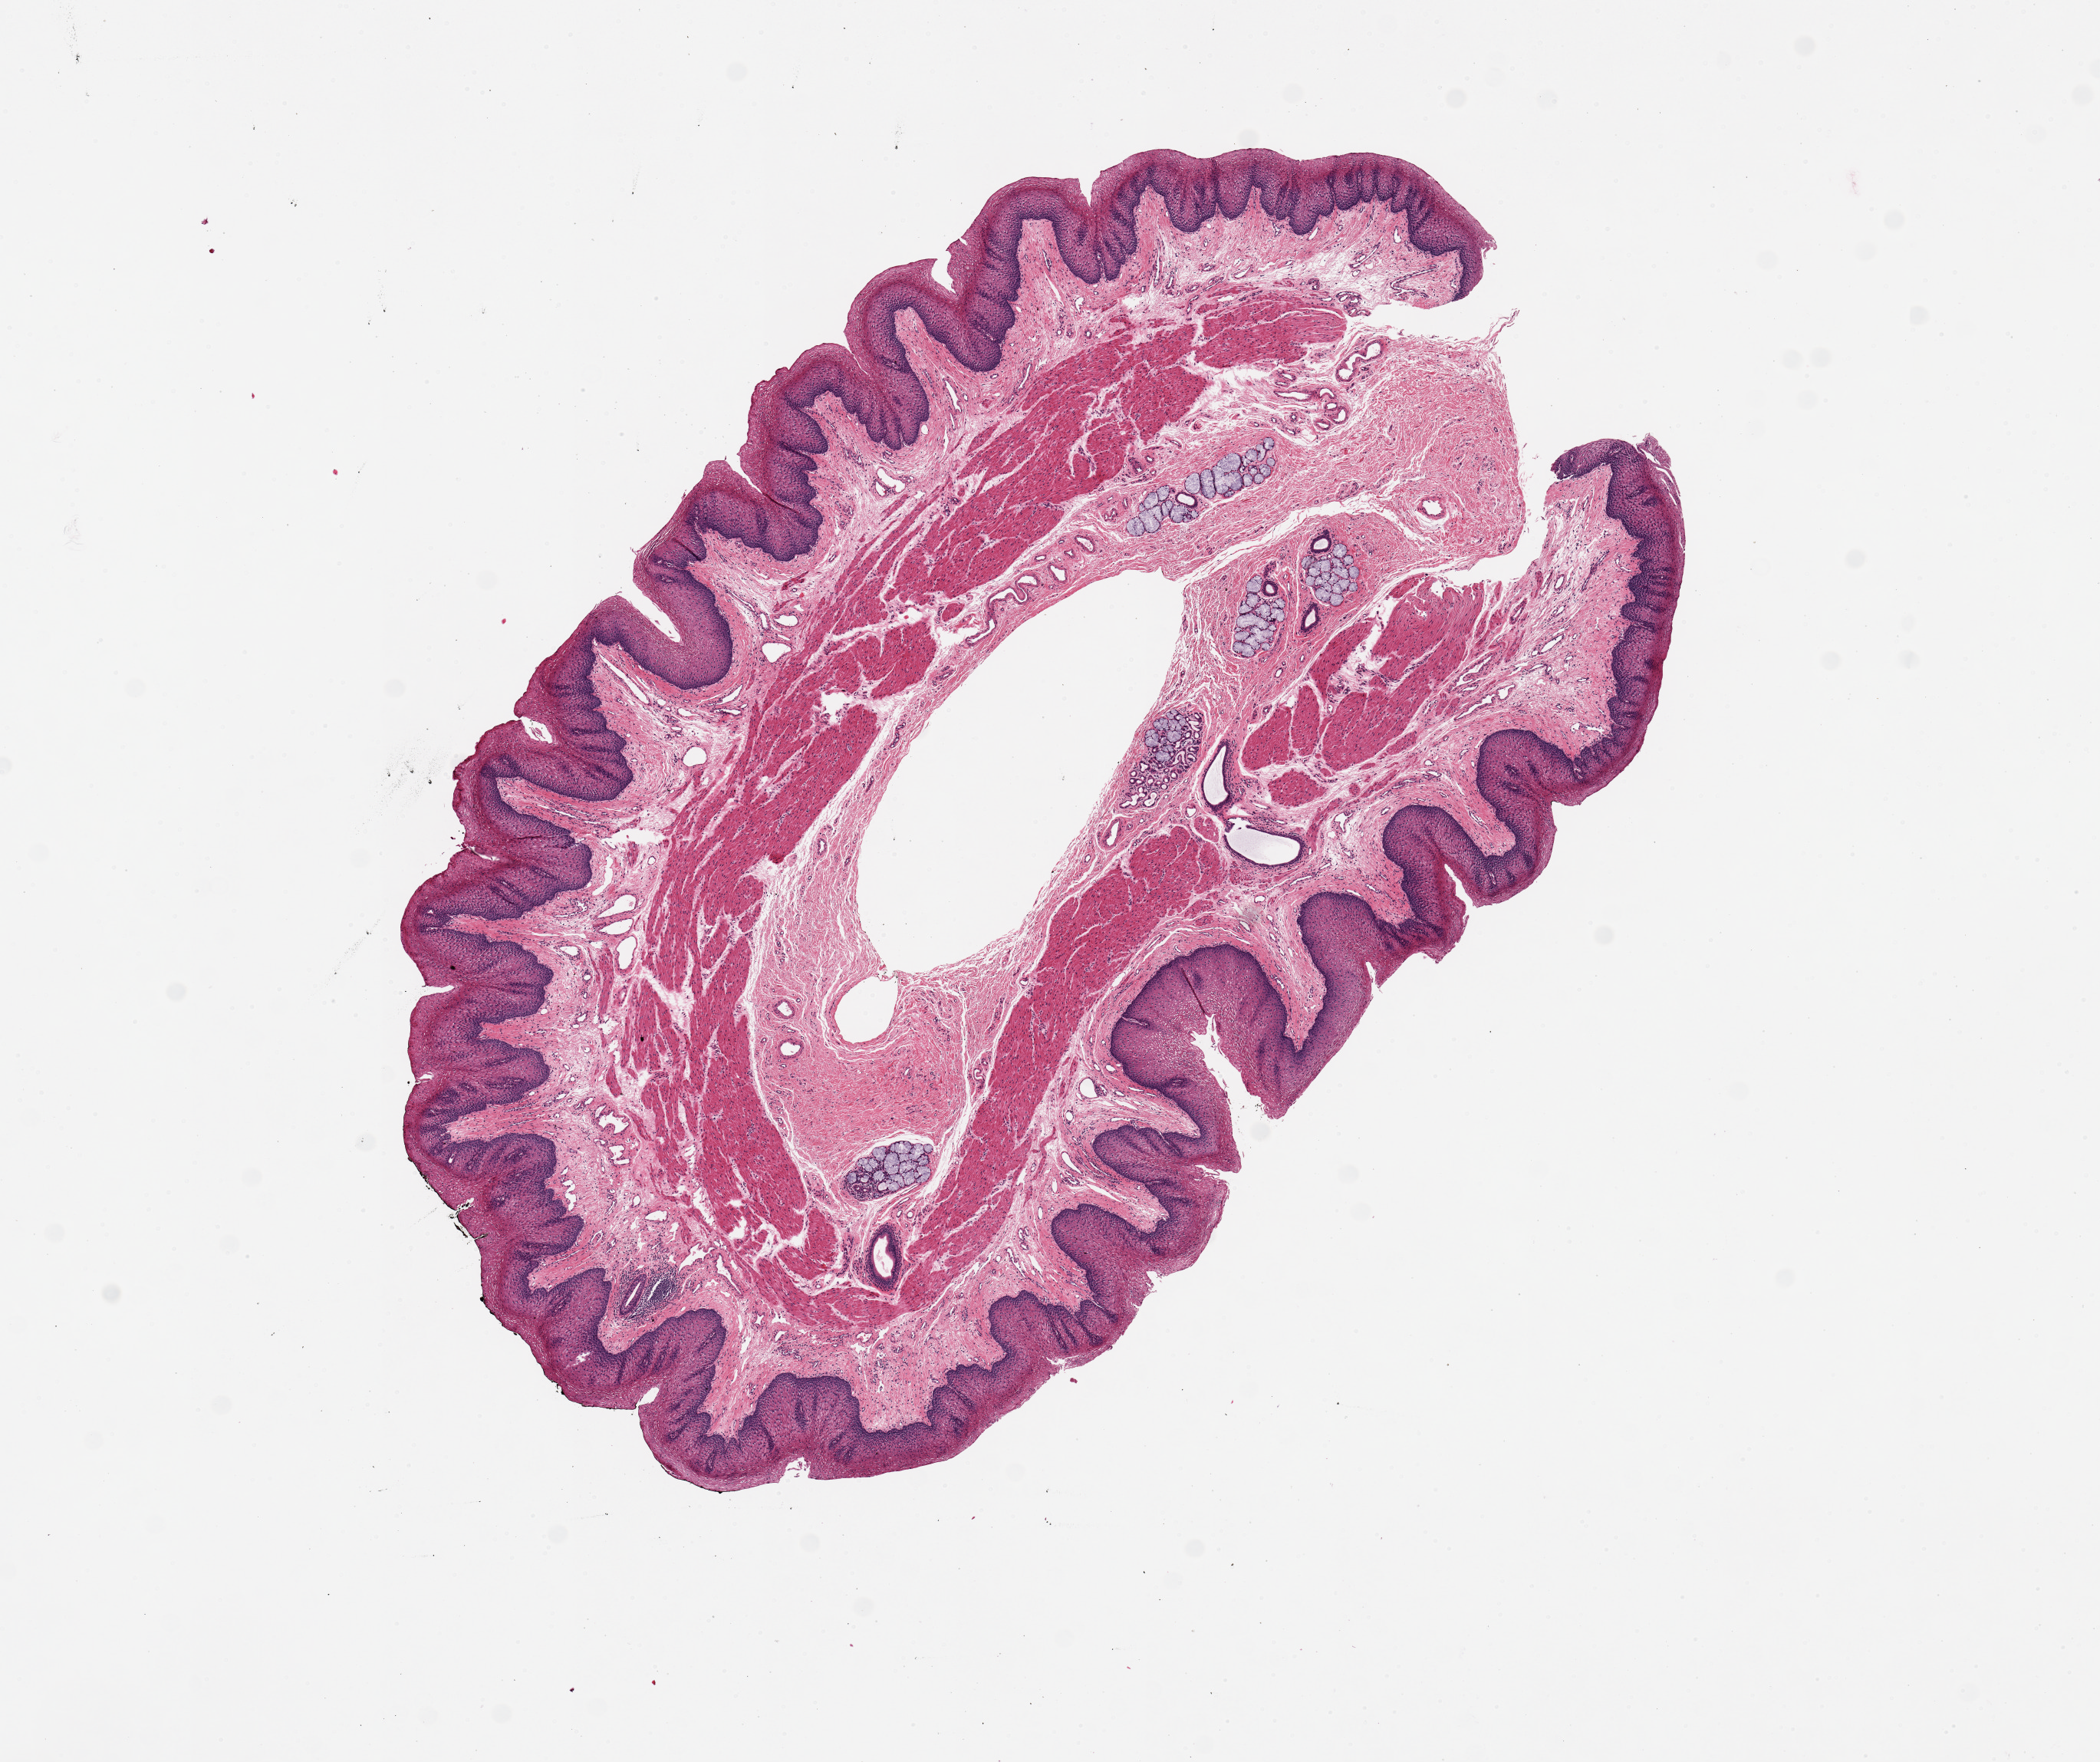
Whole-slide image, H&E stain — shown as a low-resolution overview of the whole scanned area (about 10.8 x 9.1 mm, acquisition: 20x scan). PAXgene-fixed, paraffin-embedded tissue. Sampled site (target tissue): esophageal mucous membrane. Tissue donor sample. Donor sex: female.
Pathologist's review note for this sample: 1 piece. 7x5mm; Well dissected: no muscularis propria.